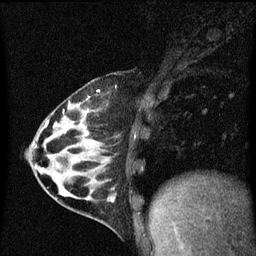
Breast MRI (dynamic contrast-enhanced), one sagittal slice. Position 22 of 60 along the scan axis. Dynamic contrast-enhanced series, image 2 of 3 at this slice position (ordered by acquisition). 1.5 T. TE 4.2 ms, TR 8.4 ms. 2 mm slice thickness. 256 × 256 image matrix, field of view 200 × 200 mm. Patient: female, 32 years.
Outlined on this slice (semi-automatically segmented with operator editing):
- analysis volume of interest (the breast-tissue region the enhancement analysis was run in; not a lesion): bounding box [x1, y1, x2, y2] px = [34, 74, 148, 169]
- tumour enhancement mask (voxels above the 70 % enhancement threshold inside the analysis volume of interest): [46, 122, 50, 127]